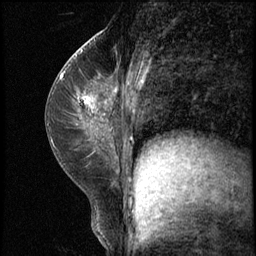
Breast MRI (dynamic contrast-enhanced), one sagittal slice; position 32 of 62 along the scan axis; 3 images stored at this slice position (order not interpretable as contrast timing); 1.5 T; TE 4.2 ms, TR 8.7 ms; 2.5 mm slice thickness; 256 × 256 image matrix, field of view 180 × 180 mm. Patient: female, 35 years. From the clinical record (not read from this slice): setting: breast cancer imaged before/during neoadjuvant chemotherapy; receptor status: HER2-positive.
Outlined on this slice (semi-automatically segmented with operator editing):
- analysis volume of interest (the breast-tissue region the enhancement analysis was run in; not a lesion): box from (x=71, y=78) to (x=120, y=139) px
- tumour enhancement mask (voxels above the 140 % enhancement threshold inside the analysis volume of interest): (x=81, y=96)–(x=94, y=108)